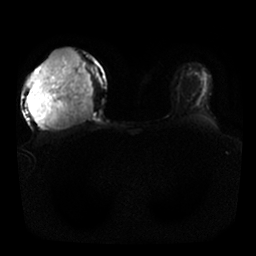
Breast MRI, one axial slice. Position 17 of 25 along the scan axis. Diffusion-weighted series; image 2 of 4 stored at this slice position (different b-values; order by instance number). 1.5 T. 4 mm slice thickness. 256 × 256 image matrix, field of view 340 × 340 mm. Female patient.
Outlined on this slice (outlined manually by an expert reader):
- tumour on diffusion-weighted imaging: box from (x=28, y=48) to (x=94, y=128) px